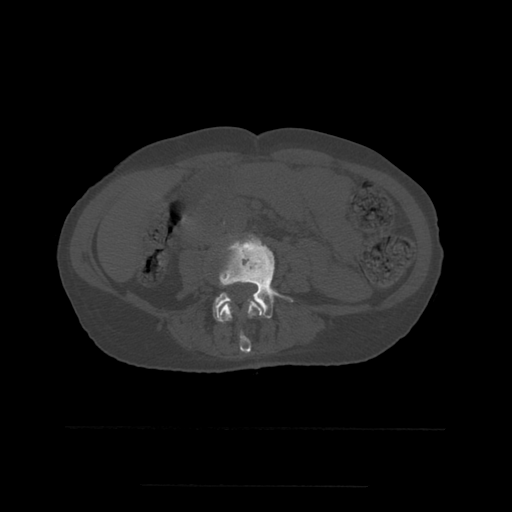
CT including the spine, one axial slice. Slice 176 of 544 in the series (ordered by position). Bone window (W 1800 / L 400 HU). 512 × 512 image matrix, field of view 350 × 350 mm. Patient age 58 years. From the clinical record (not read from this slice): primary cancer: lung.
Outlined on this slice (semi-automatic segmentation, software-assisted and operator-edited):
- L3 vertebra: bounding box [x1, y1, x2, y2] px = [218, 300, 262, 354]
- L4 vertebra: [213, 235, 293, 322]